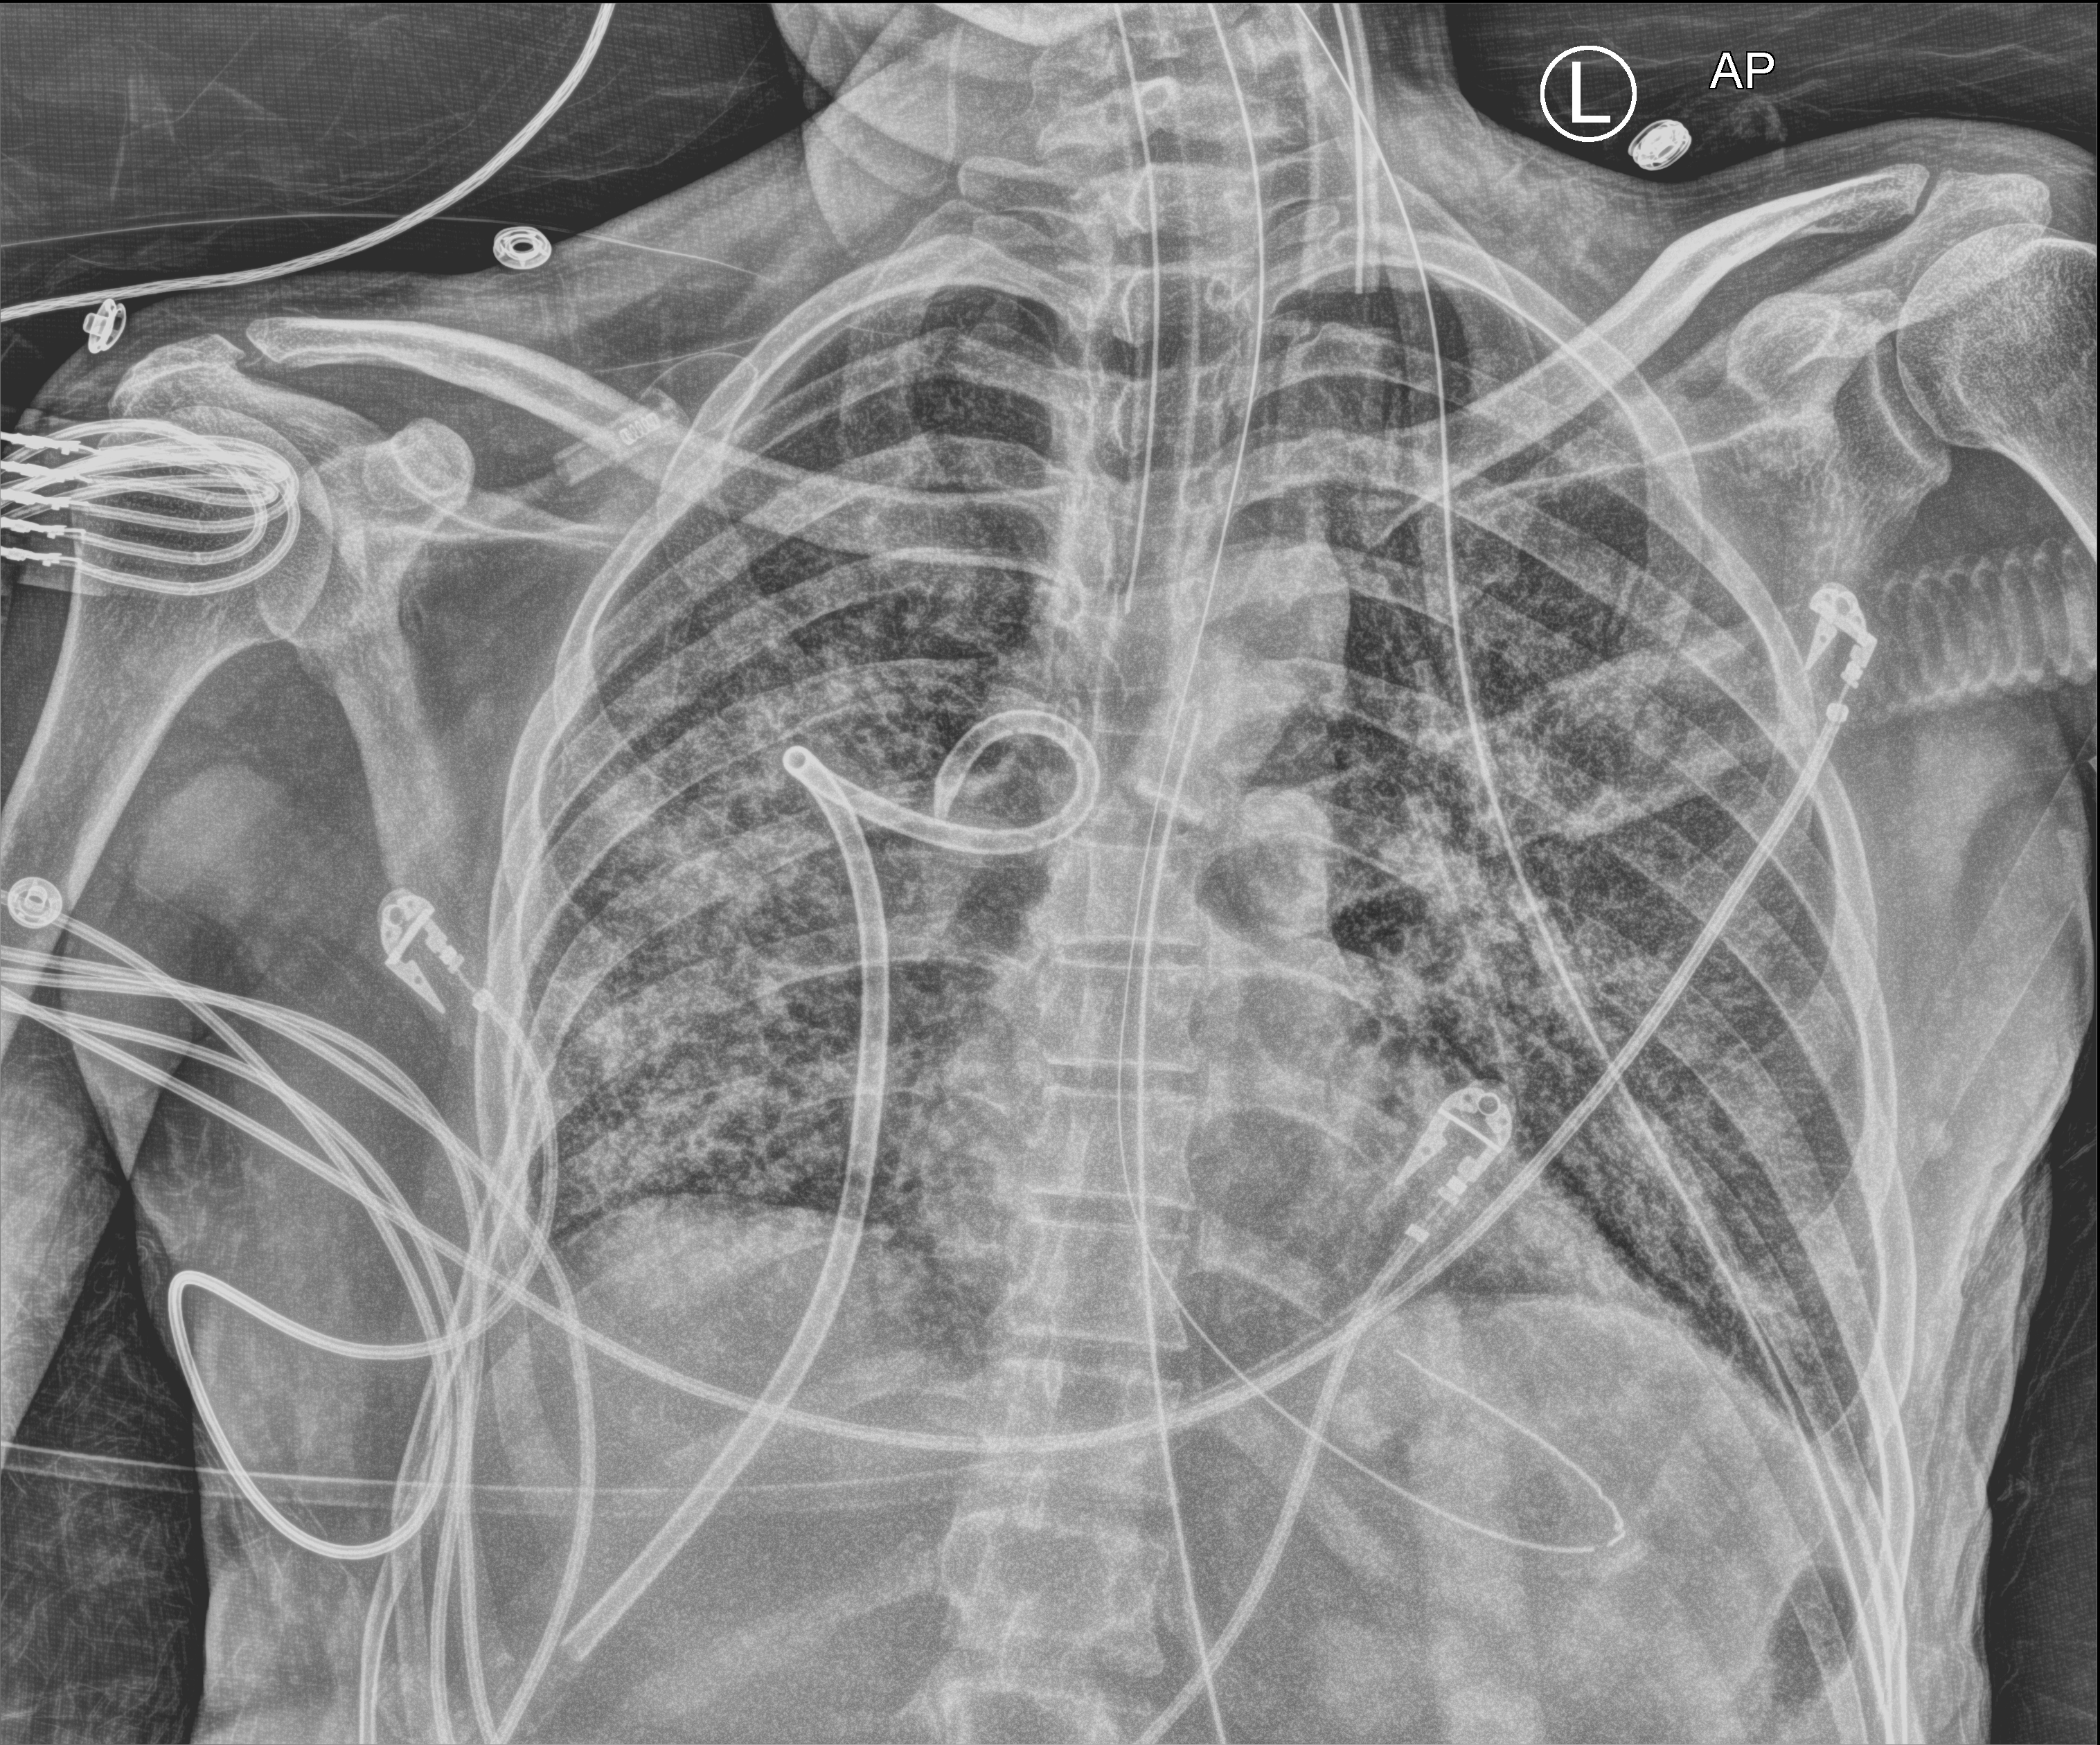
Bedside chest radiograph (computed radiography). Patient hospitalised with COVID-19, aged 18–59 years.
From the hospital-stay record, not from the radiograph (when in the stay this image was taken is not recorded):
- other chronic lung disease (admission record): no
- mechanically ventilated during this hospital stay: yes